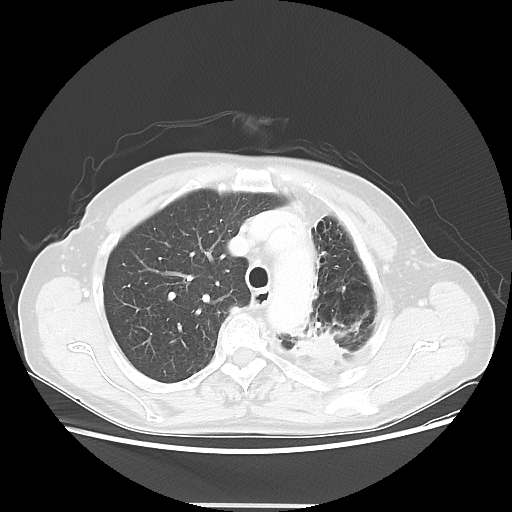
Chest CT, one axial slice. Slice 40 of 56 in the series (ordered by position). 100 kVp. Lung window (W 1500 / L -600 HU). 5 mm slice thickness. 512 × 512 image matrix. Patient: female, 63 years. Case-level facts recorded for this patient, not image findings: clinical TNM (as recorded): T2a N0 M0.
Outlined on this slice (bounding box drawn by a radiologist):
- lung tumour (recorded histology: adenocarcinoma): bounding box [x1, y1, x2, y2] px = [300, 328, 344, 368]